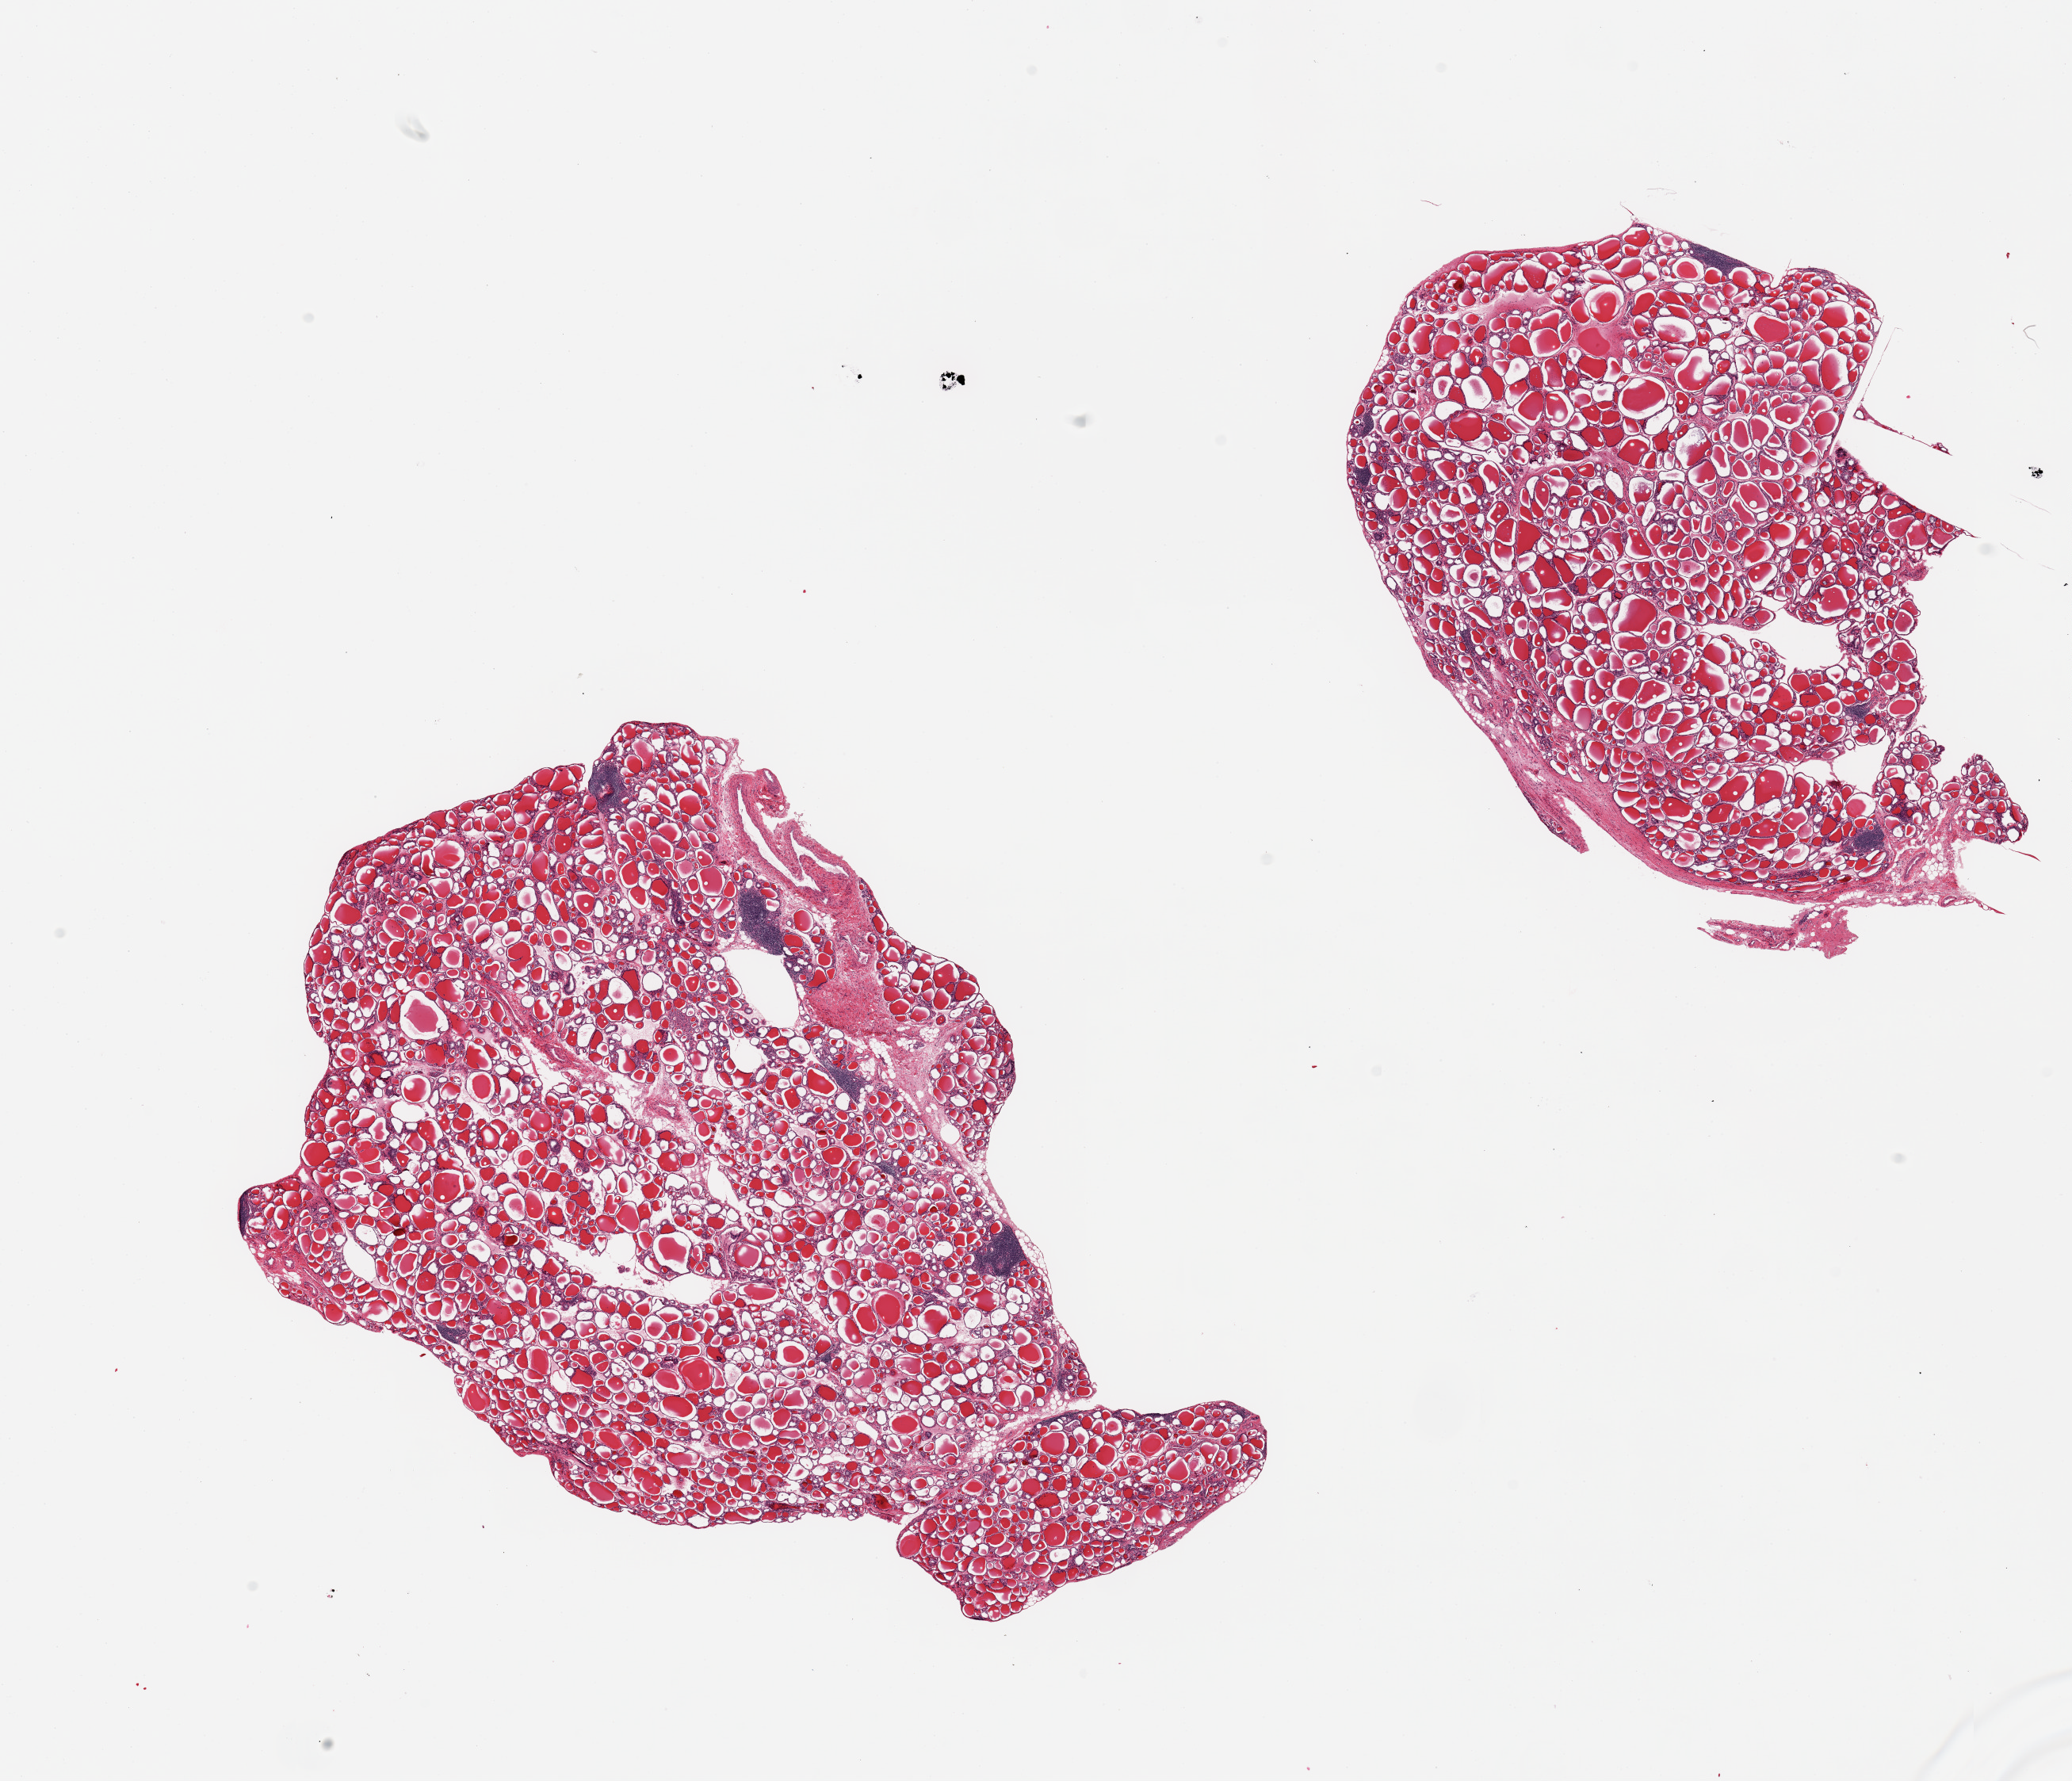
Hematoxylin and eosin (H&E) whole-slide image, shown as a low-resolution overview of the whole scanned area (about 20.7 x 17.8 mm). PAXgene-fixed paraffin-embedded (PFPE) section. Section of thyroid (target tissue). Tissue donor sample. Donor: female.
Reviewer comment on this tissue sample: 2 pieces; several lymphocytic aggregates, ? Hashimoto thyroiditis.